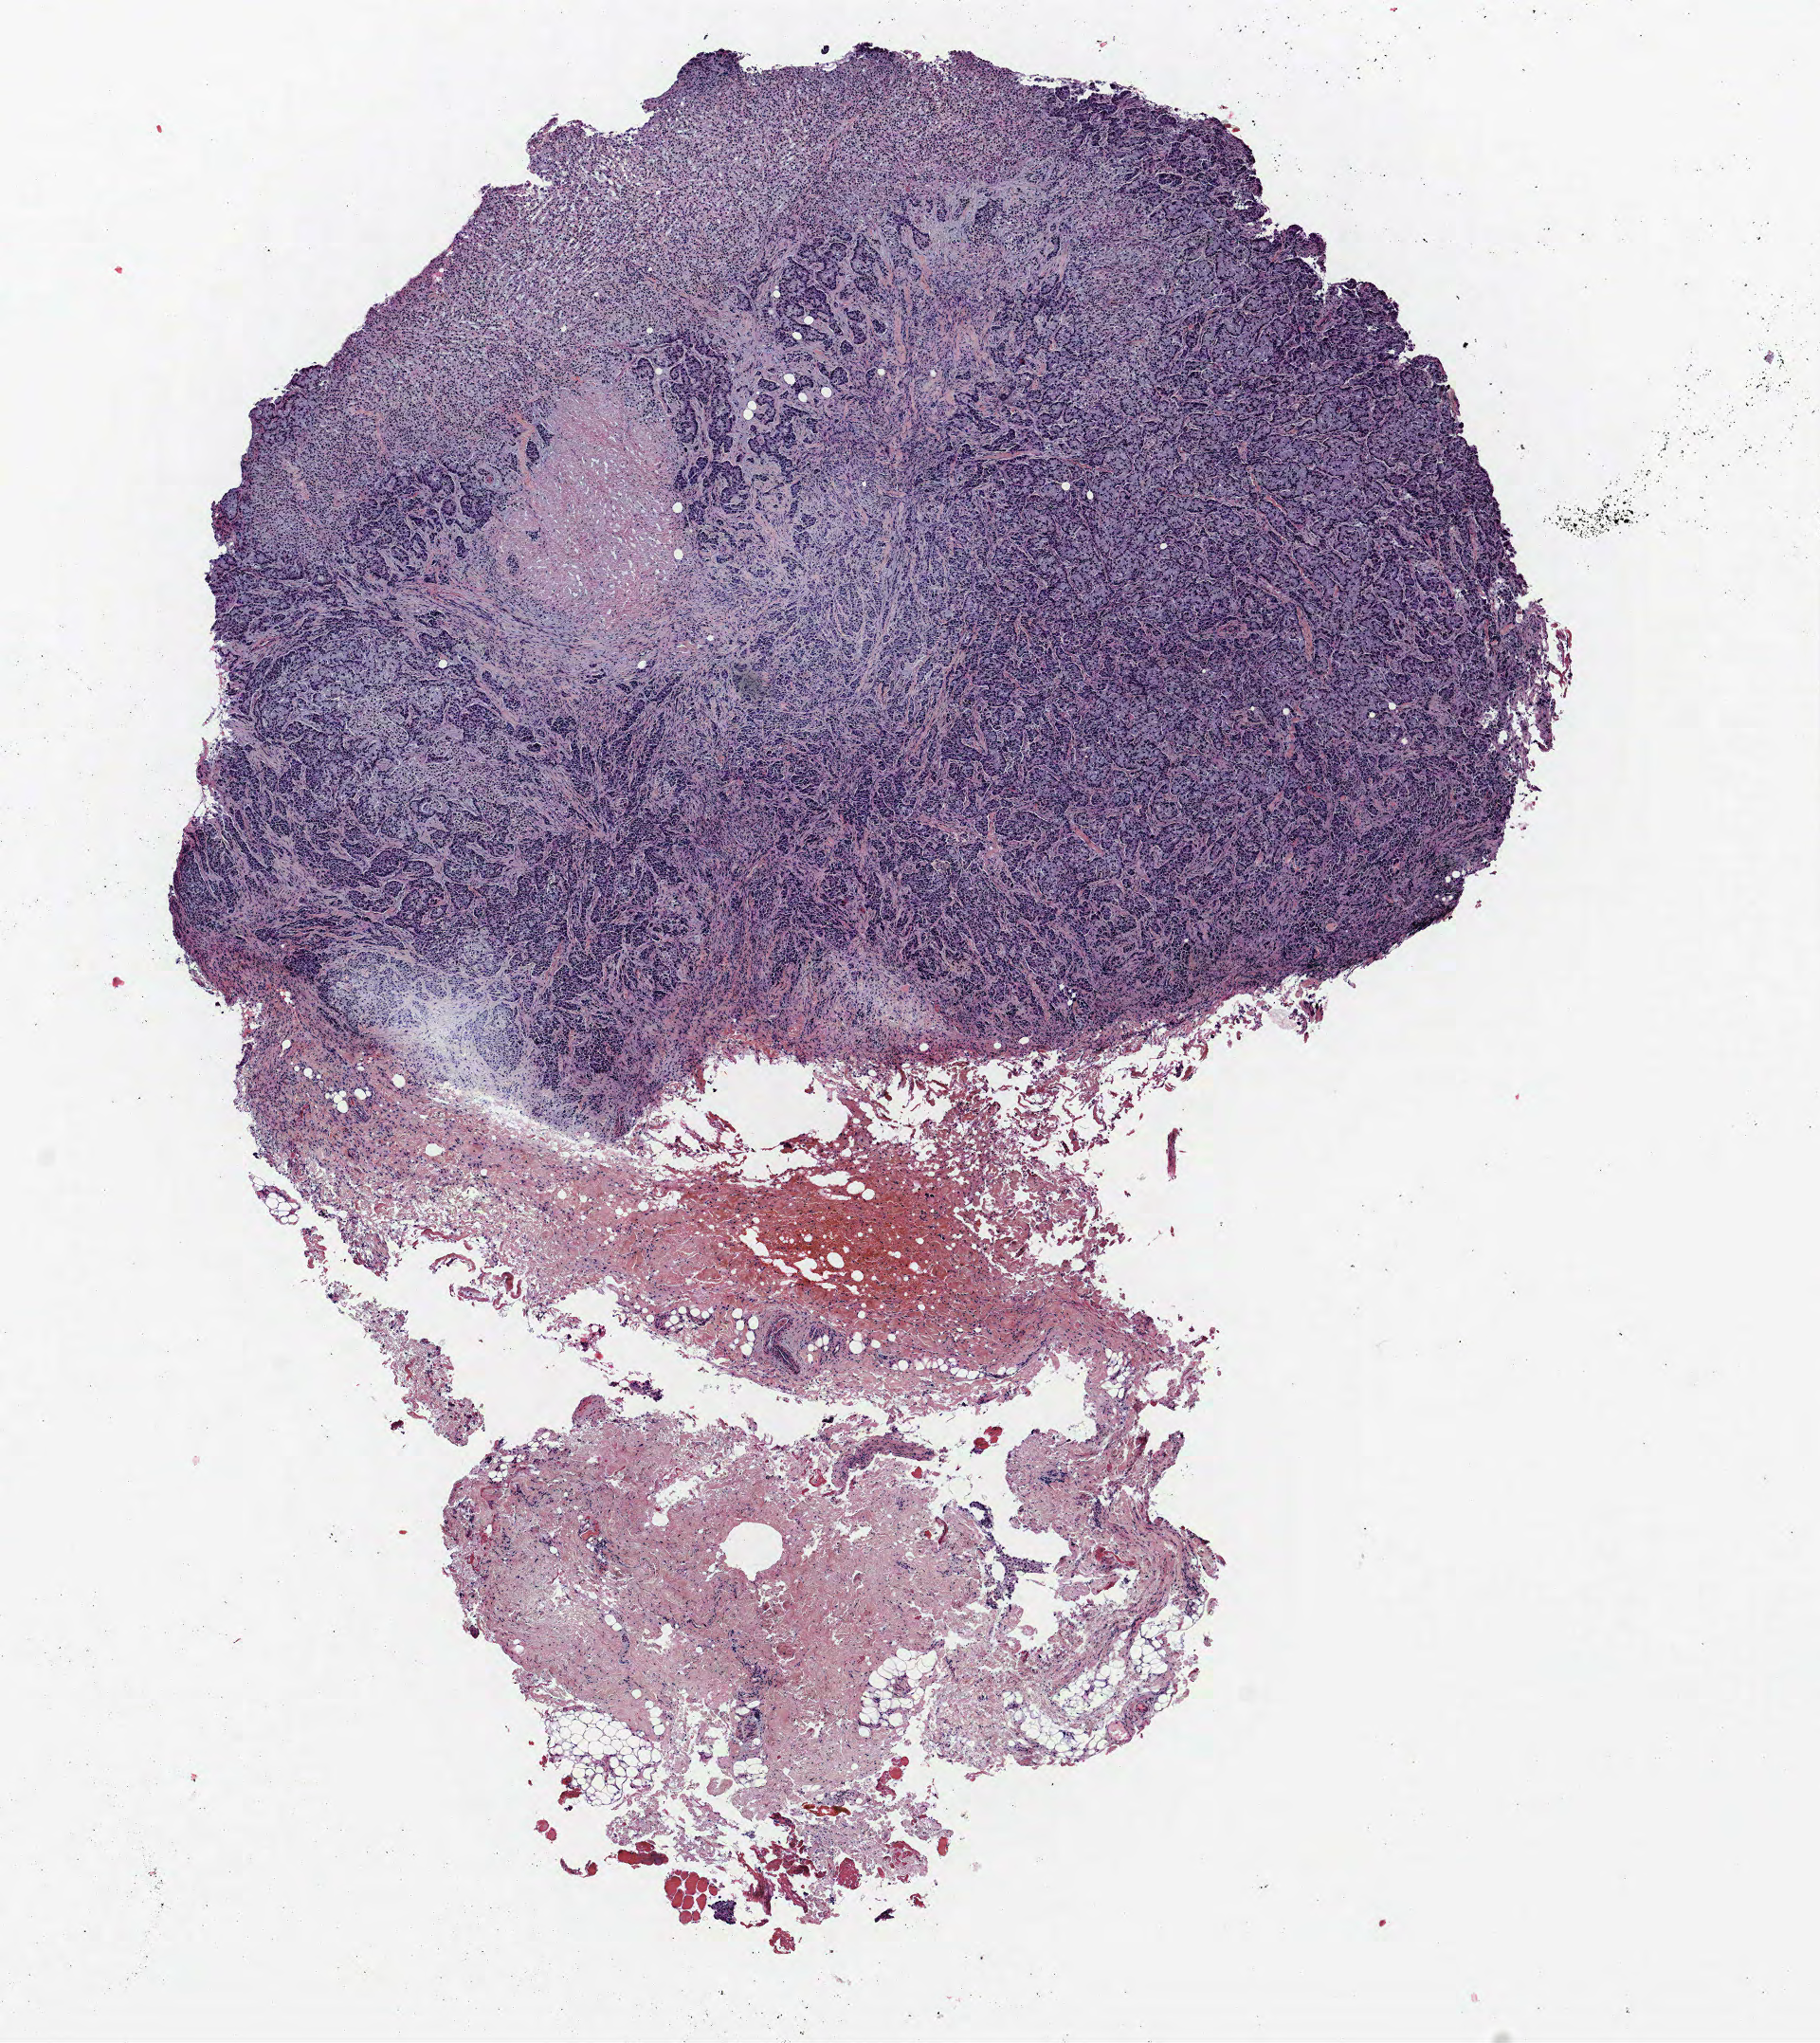
H&E whole-slide image — shown as a low-resolution overview of the whole scanned area (about 7.7 x 8.6 mm, slide scanned at 40x), FFPE section, lung tissue. Male patient, aged 62 at enrolment. Current smoker at enrolment. Grade: moderately differentiated (G2).
* ICD-O-3 topography: lower lobe of lung (C34.3)
* primary tumour location (clinical record): right lower lobe
* stage (AJCC 6th edition): IV
* participant's lung-cancer diagnosis: Adenocarcinoma, NOS